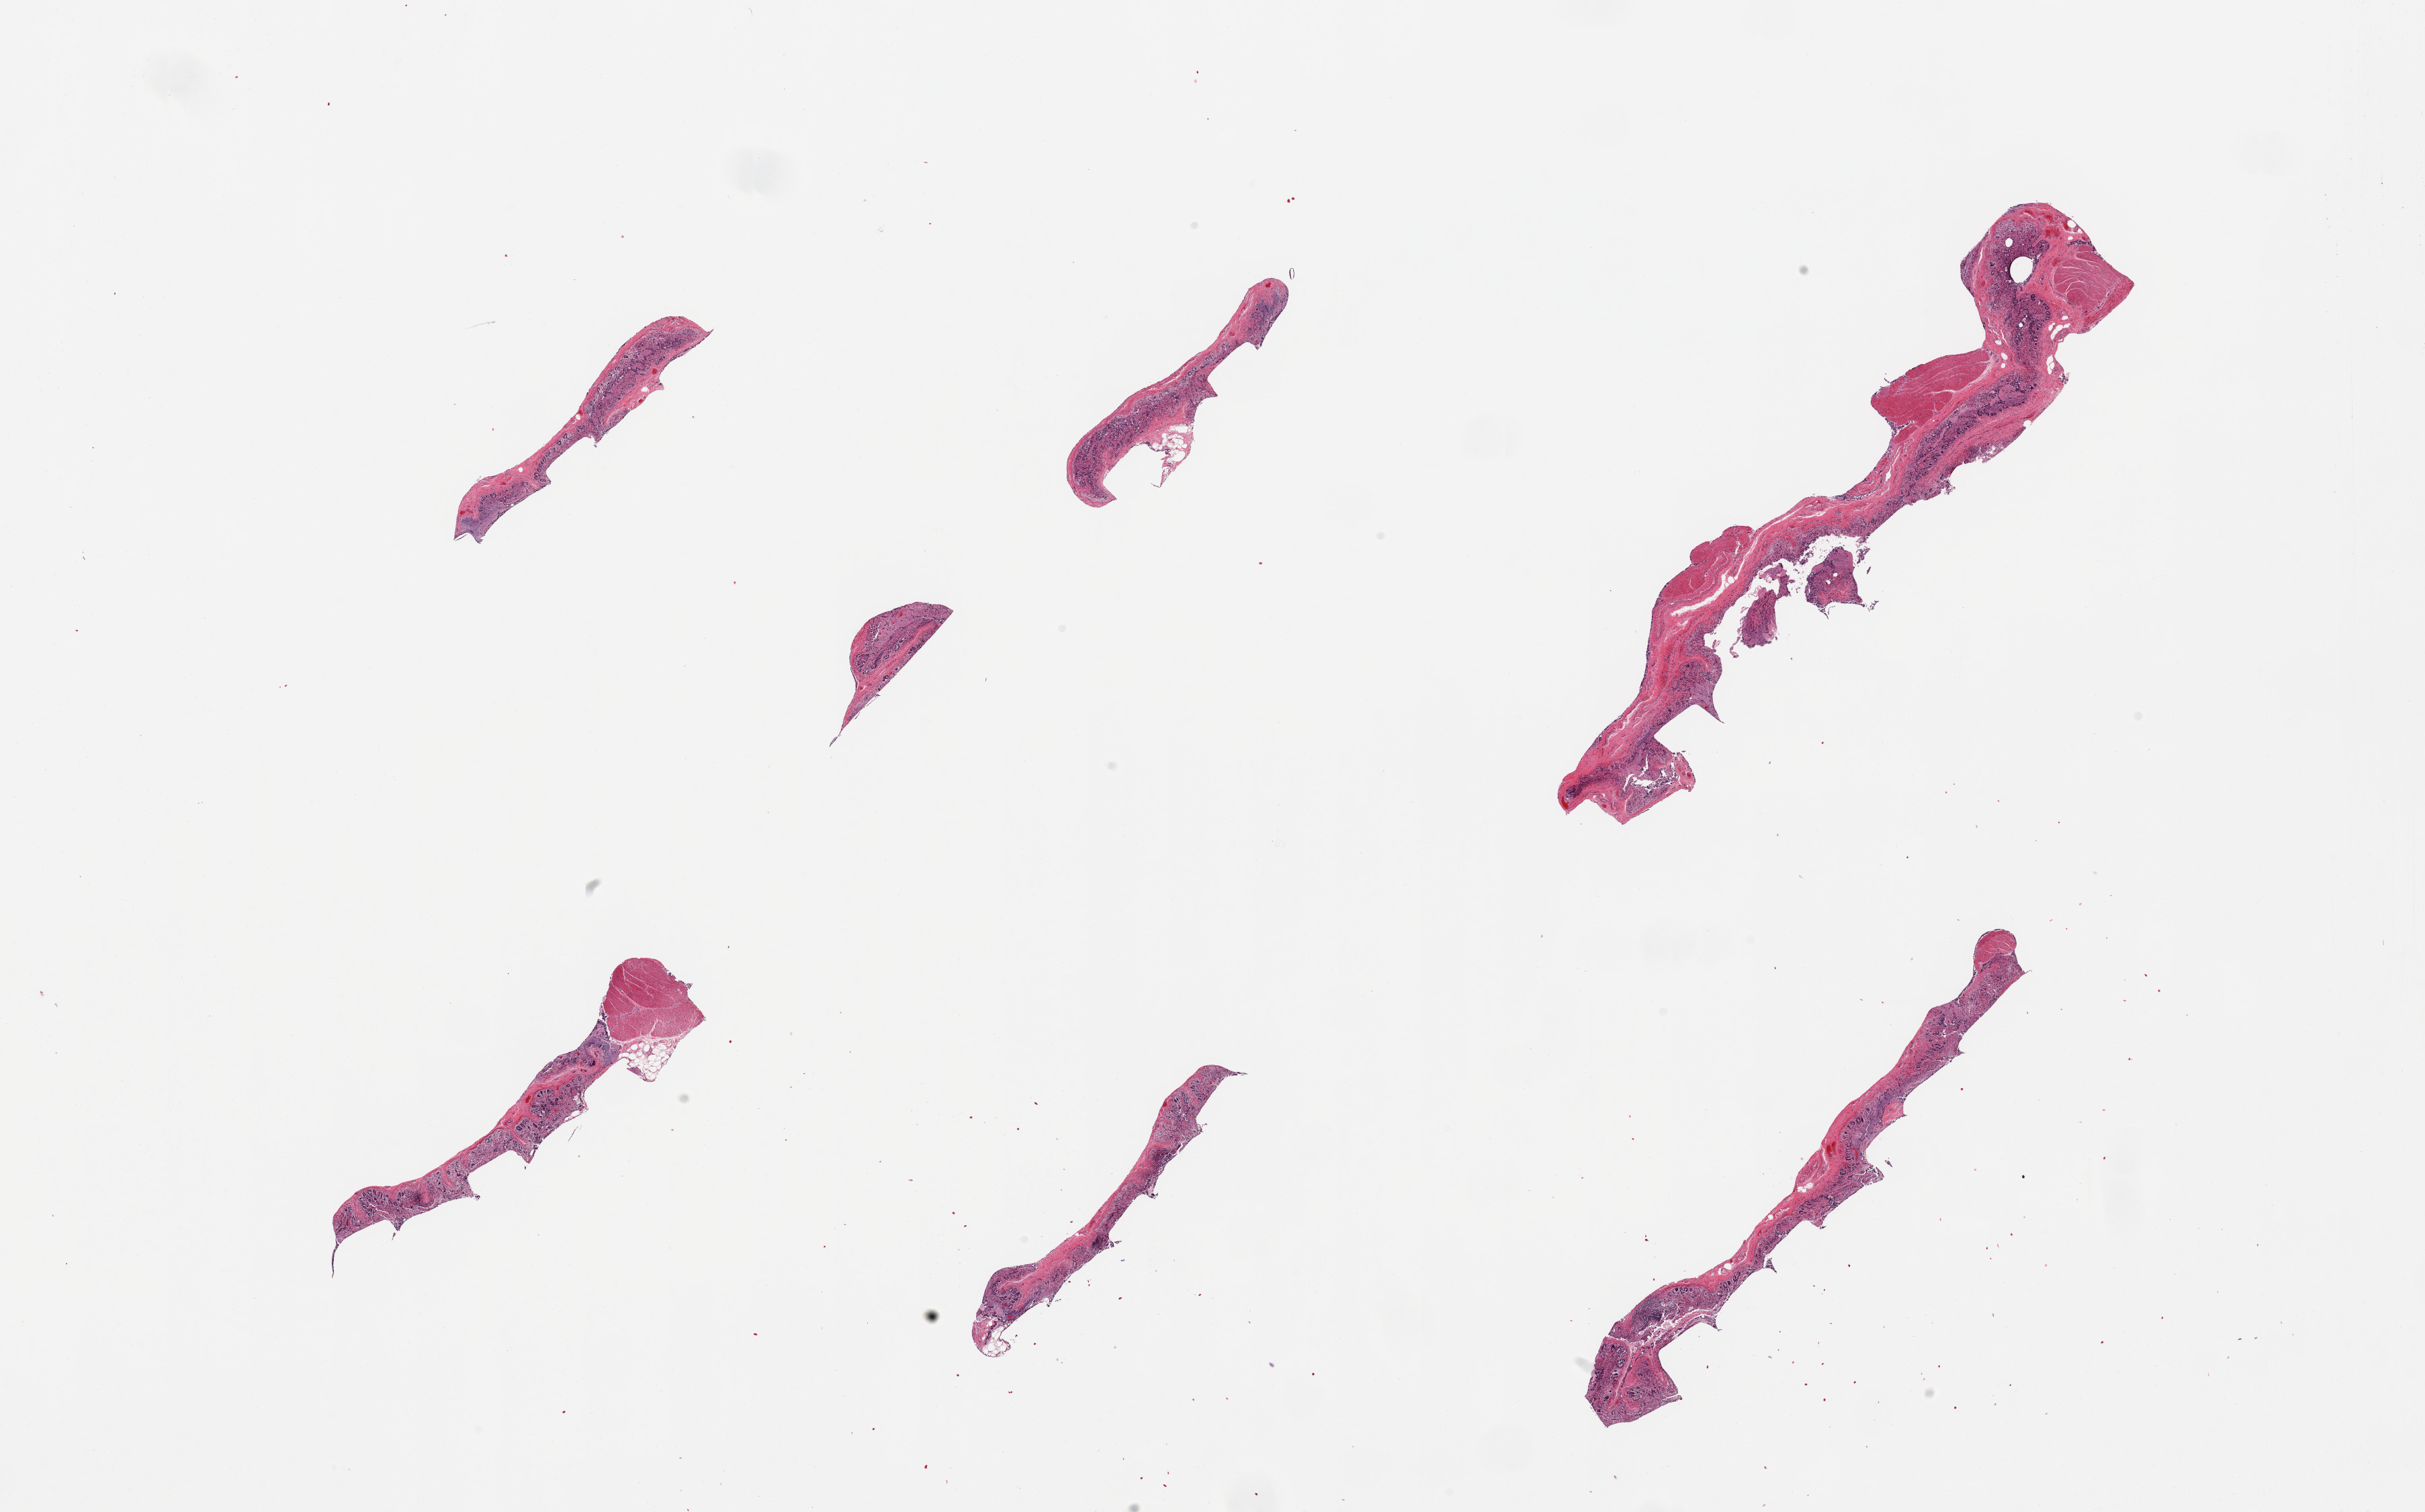
Whole-slide image, haematoxylin and eosin stain — low-resolution overview of the scanned area, about 28.5 x 17.8 mm. PAXgene-fixed, paraffin-embedded tissue. Target tissue: transverse colon. Donor tissue sample. Male donor.
Reviewer comment on this tissue sample: 6 pieces, mucosa with advance autolysis/sloughed.